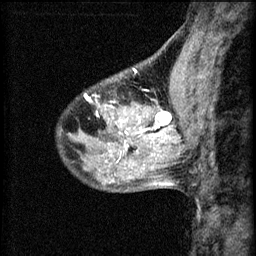
Breast MRI (dynamic contrast-enhanced), one sagittal slice. Position 23 of 60 along the scan axis. 3 images stored at this slice position (order not interpretable as contrast timing). 1.5 T. TE 4.2 ms, TR 8.2 ms. 2.2 mm slice thickness. 256 × 256 image matrix. Patient: female, 40 years.
Annotated regions visible in this slice (semi-automatic segmentation, software-assisted and operator-edited):
- analysis volume of interest (the breast-tissue region the enhancement analysis was run in; not a lesion): bounding box <108,82,175,139> (left, top, right, bottom; pixels)
- tumour enhancement mask (voxels above the 70 % enhancement threshold inside the analysis volume of interest): <112,106,173,137>